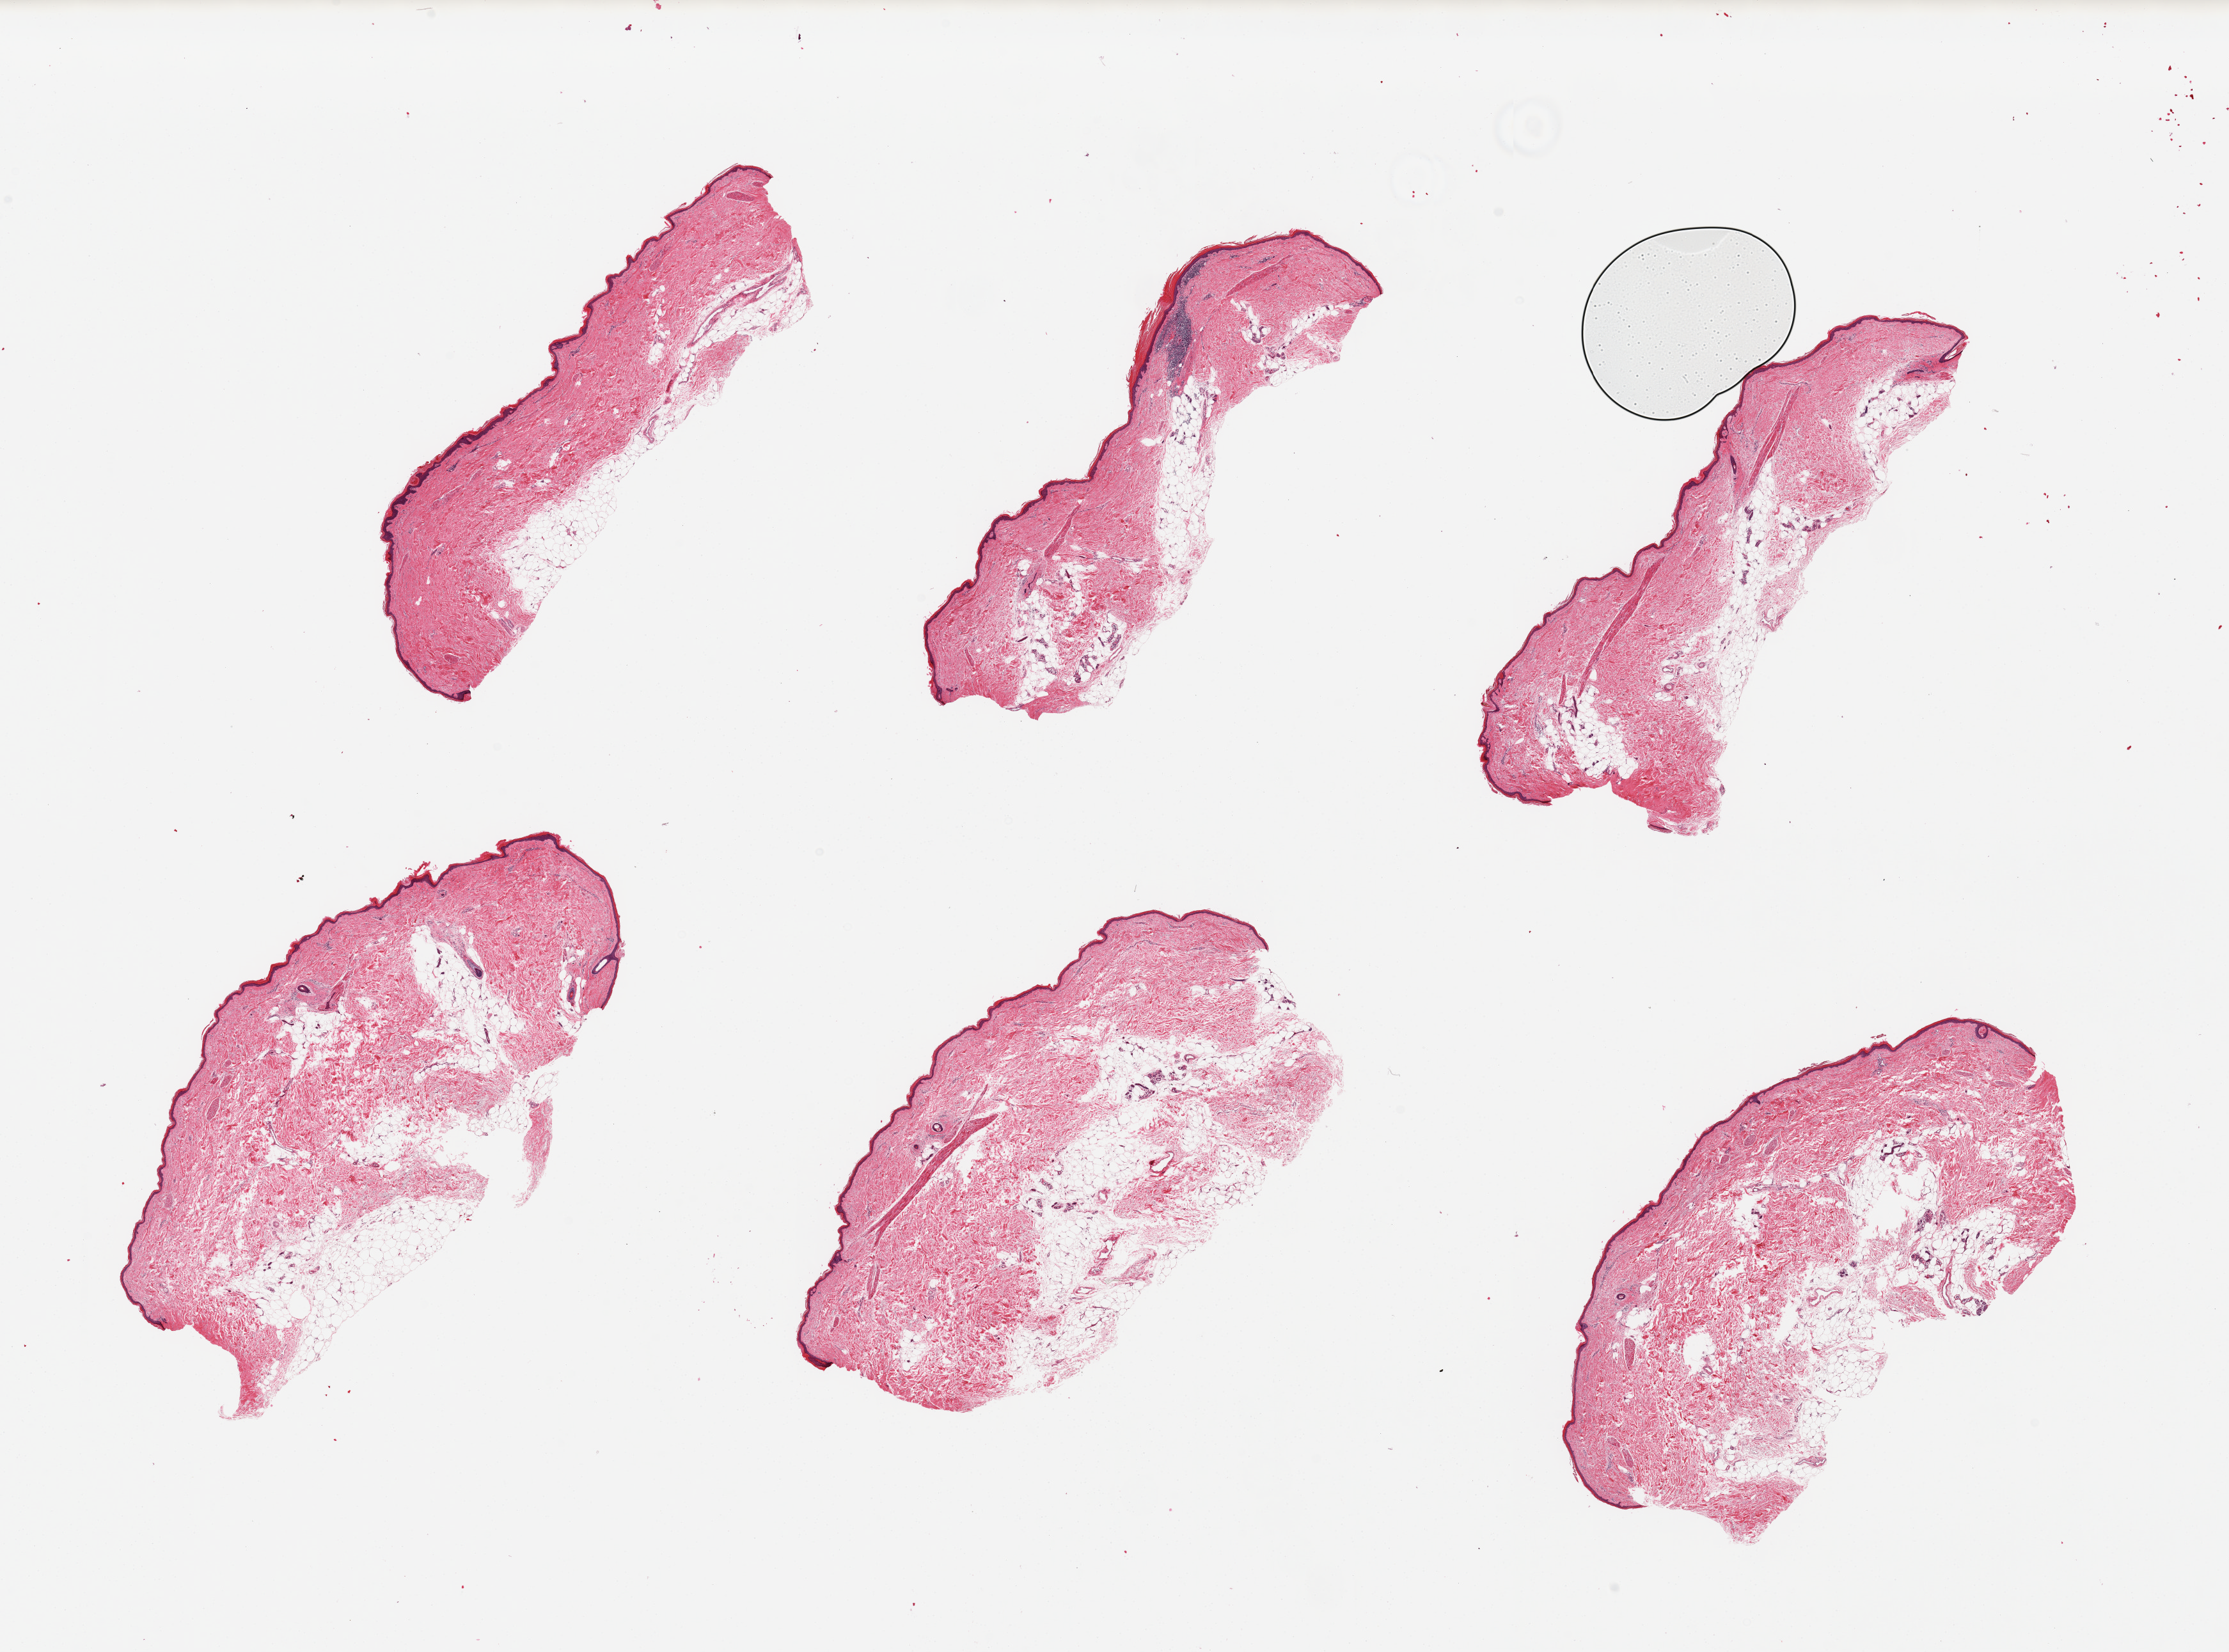
Digitized hematoxylin and eosin (H&E)-stained section, whole scanned area (about 27.6 x 20.4 mm) shown as a low-resolution overview; PAXgene-fixed, paraffin-embedded tissue; section of skin of lower leg (target tissue); donor tissue sample. Female donor.
Pathologist's review note for this sample: 6 pieces; 10-30% subcutaneous fat.